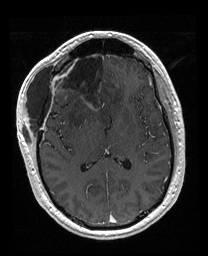
Brain MRI from a brain-tumour surgery series, one axial slice; slice 90 of 176 in the series (ordered by position); T1-weighted post-contrast; 1 mm slice thickness; 208 × 256 image matrix, field of view 208 × 256 mm. Case-level facts recorded for this patient, not image findings: histopathology: Astrocytoma; WHO grade: 4; IDH mutation: yes.
Annotated regions visible in this slice (outlined manually by an expert reader):
- previous resection cavity: box from (x=56, y=52) to (x=106, y=111) px